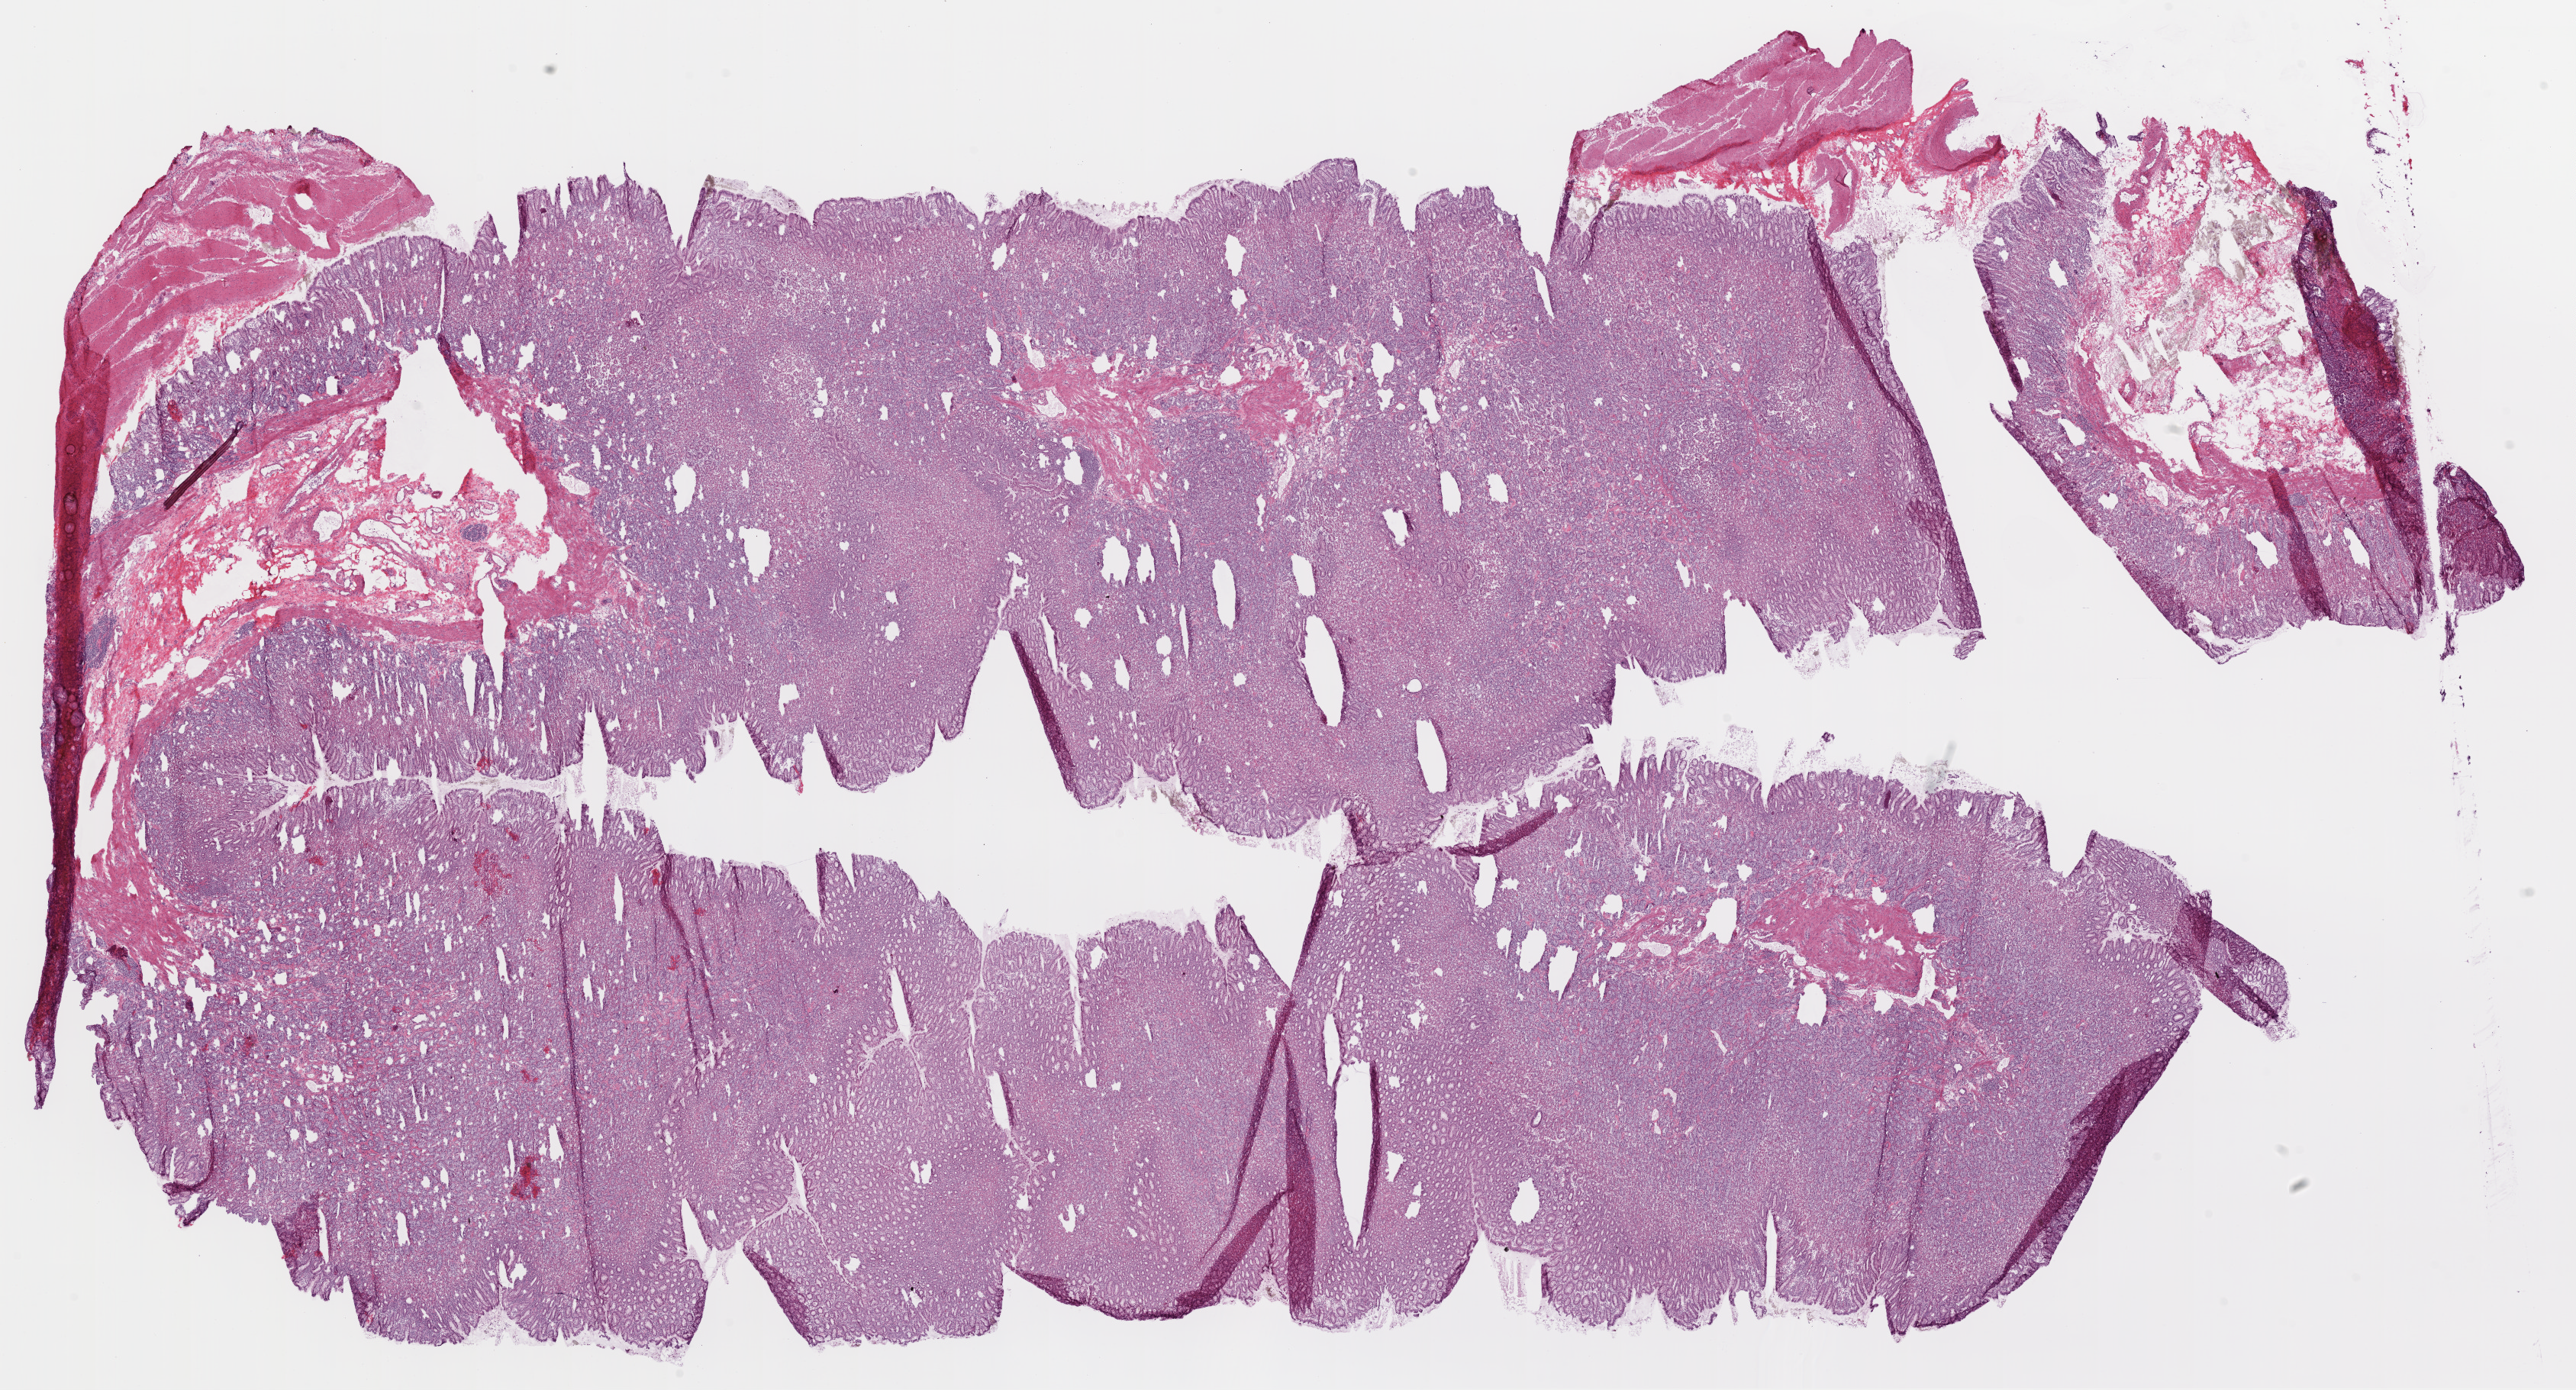
Digitized H&E-stained tissue section (whole slide) — low-resolution overview of the scanned area, about 27.1 x 14.6 mm (acquisition: 20x scan). Frozen section. Sample: solid tissue normal (non-tumour tissue), stomach. Male, age 56 years at initial diagnosis.
This section: solid tissue normal sample (biorepository sample class). Patient diagnosis: Adenocarcinoma, NOS.